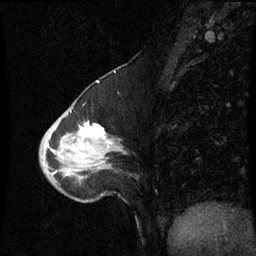
Breast MRI (dynamic contrast-enhanced), one sagittal slice; position 24 of 60 along the scan axis; dynamic contrast-enhanced series, image 2 of 3 at this slice position (ordered by acquisition); 1.5 T; TE 4.2 ms, TR 8.9 ms; 256 × 256 image matrix. Female patient, age 50 years. From the clinical record (not read from this slice): setting: breast cancer imaged before/during neoadjuvant chemotherapy; receptor status: HR-positive, HER2-negative.
Annotated regions visible in this slice (semi-automatic segmentation, software-assisted and operator-edited):
- analysis volume of interest (the breast-tissue region the enhancement analysis was run in; not a lesion): box from (x=41, y=98) to (x=126, y=203) px
- tumour enhancement mask (voxels above the 70 % enhancement threshold inside the analysis volume of interest): (x=79, y=124)–(x=111, y=143)